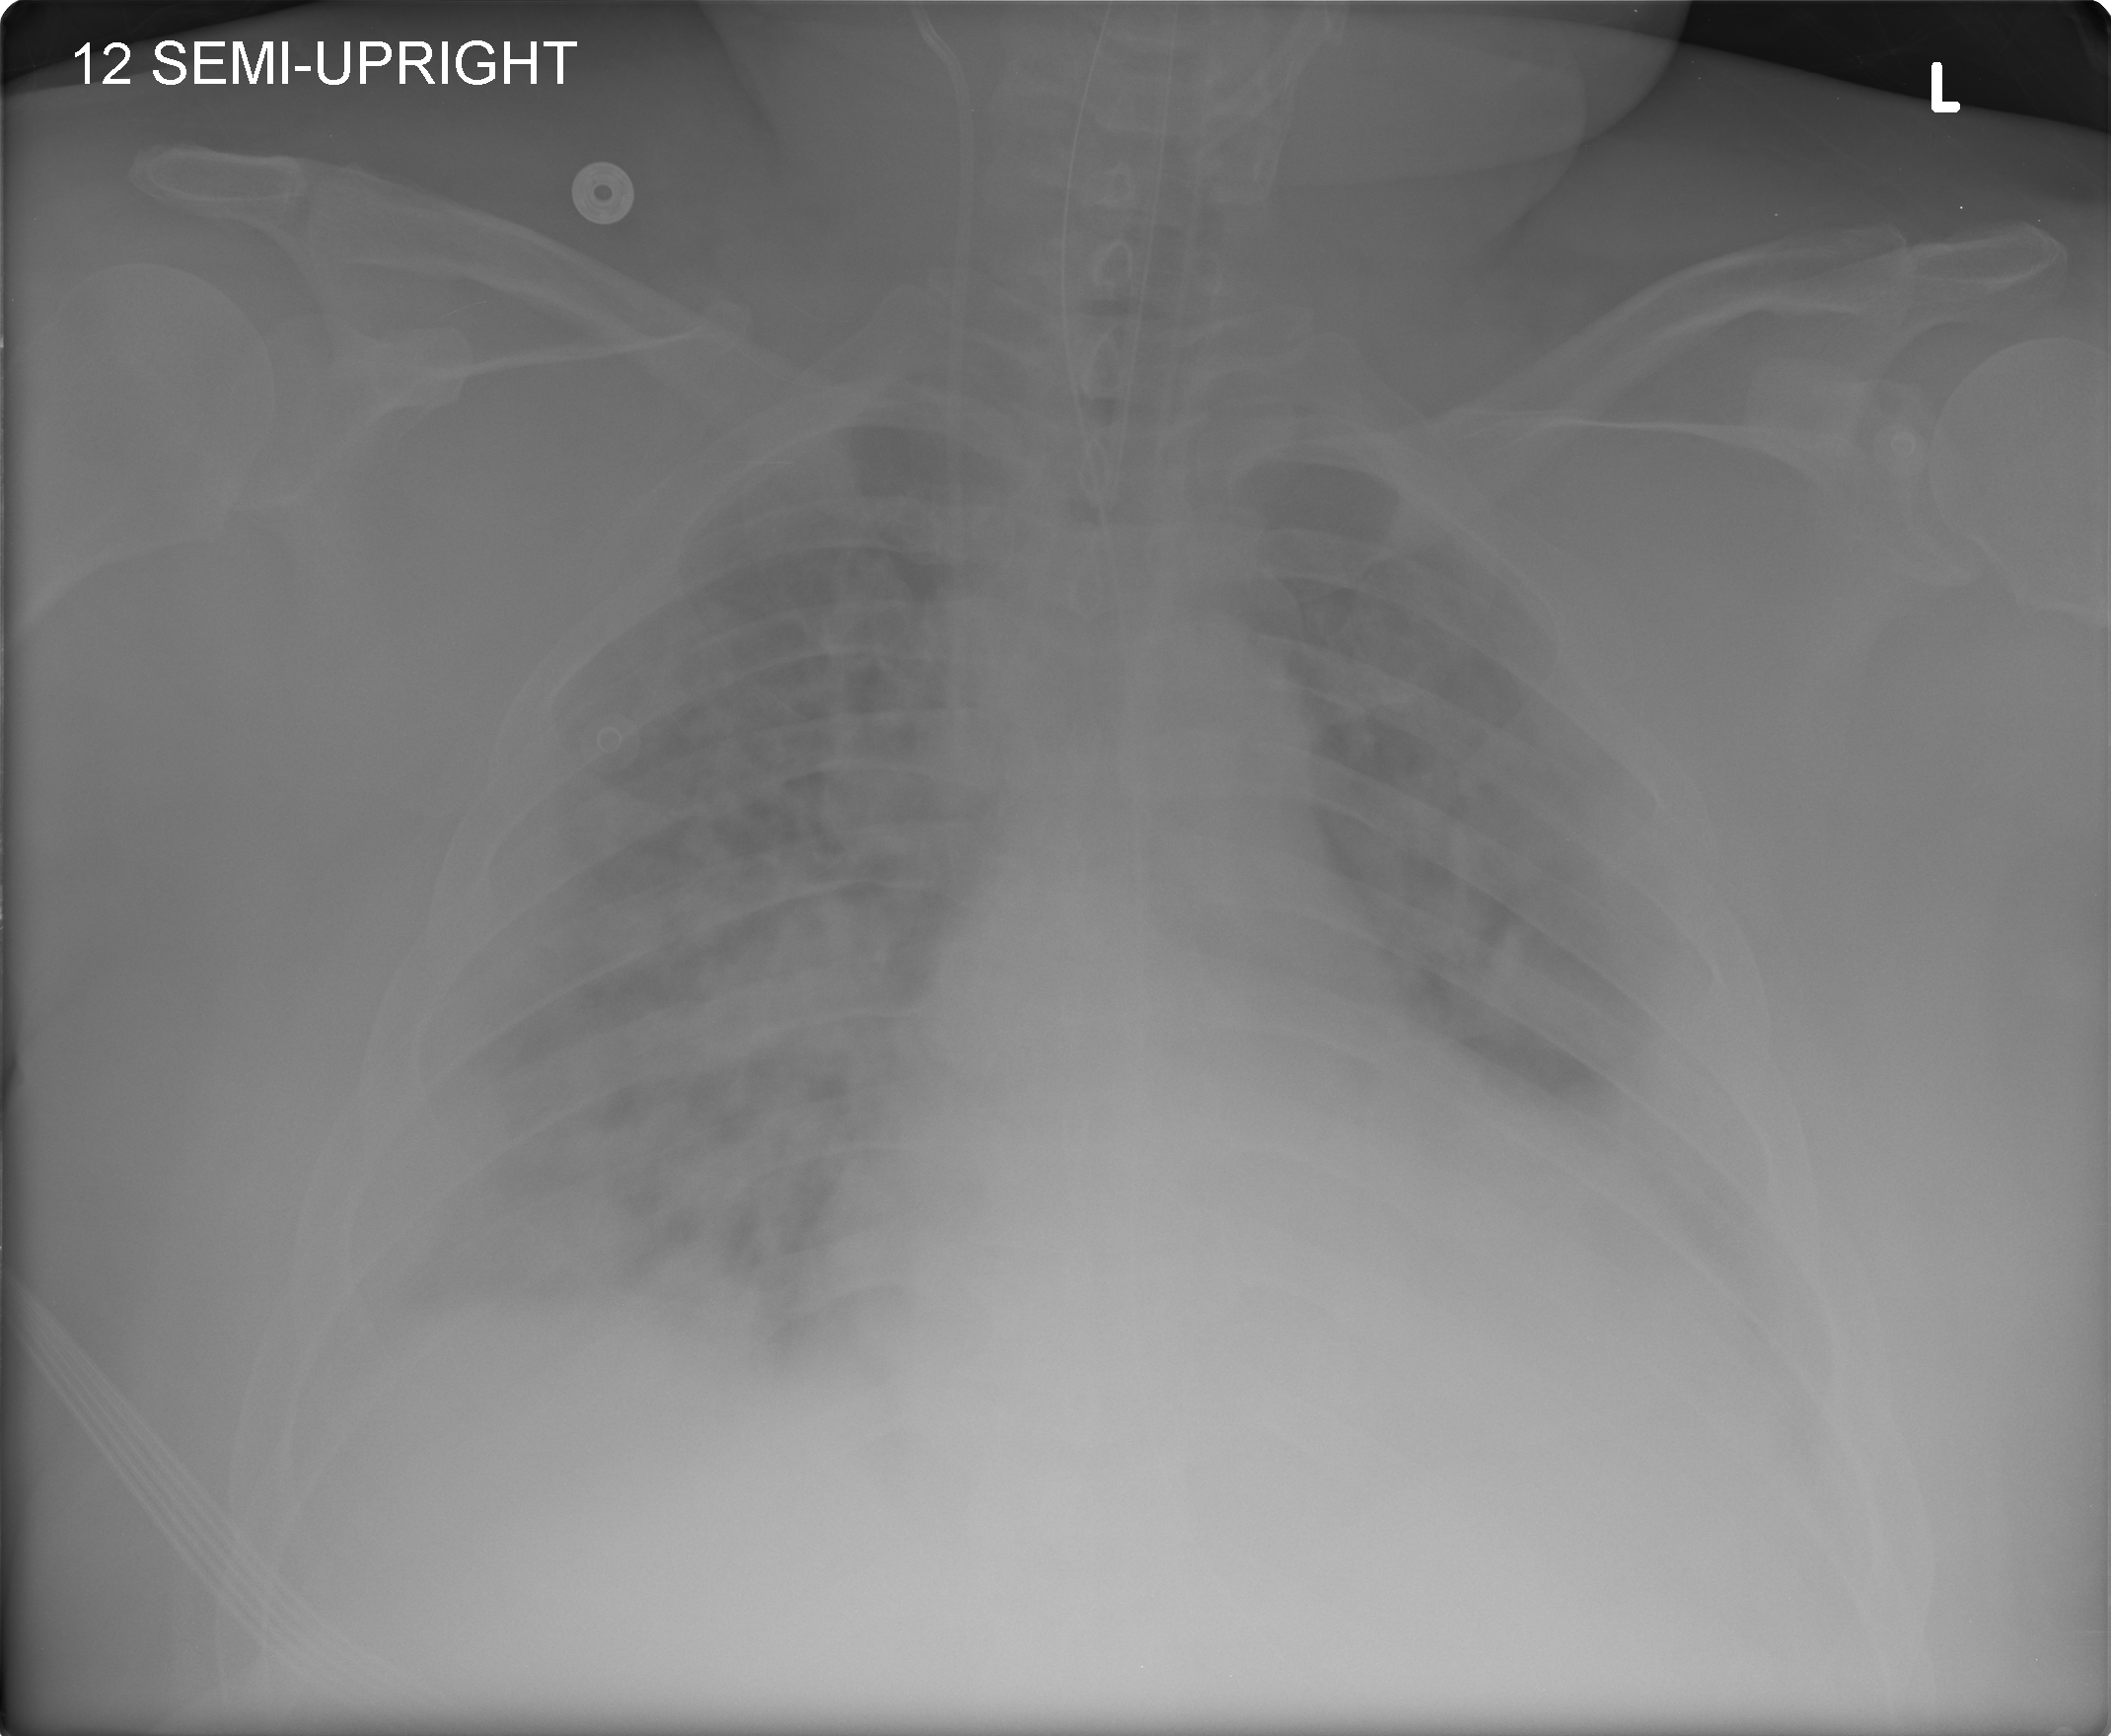
Chest X-ray (portable), AP projection. Male patient, age 55 years; imaged 1 day after the COVID-19 diagnosis.
Radiologist key findings (as recorded): Diffuse bilateral peribronchovascular opacities throughout both lungs, worsened since recent prior.